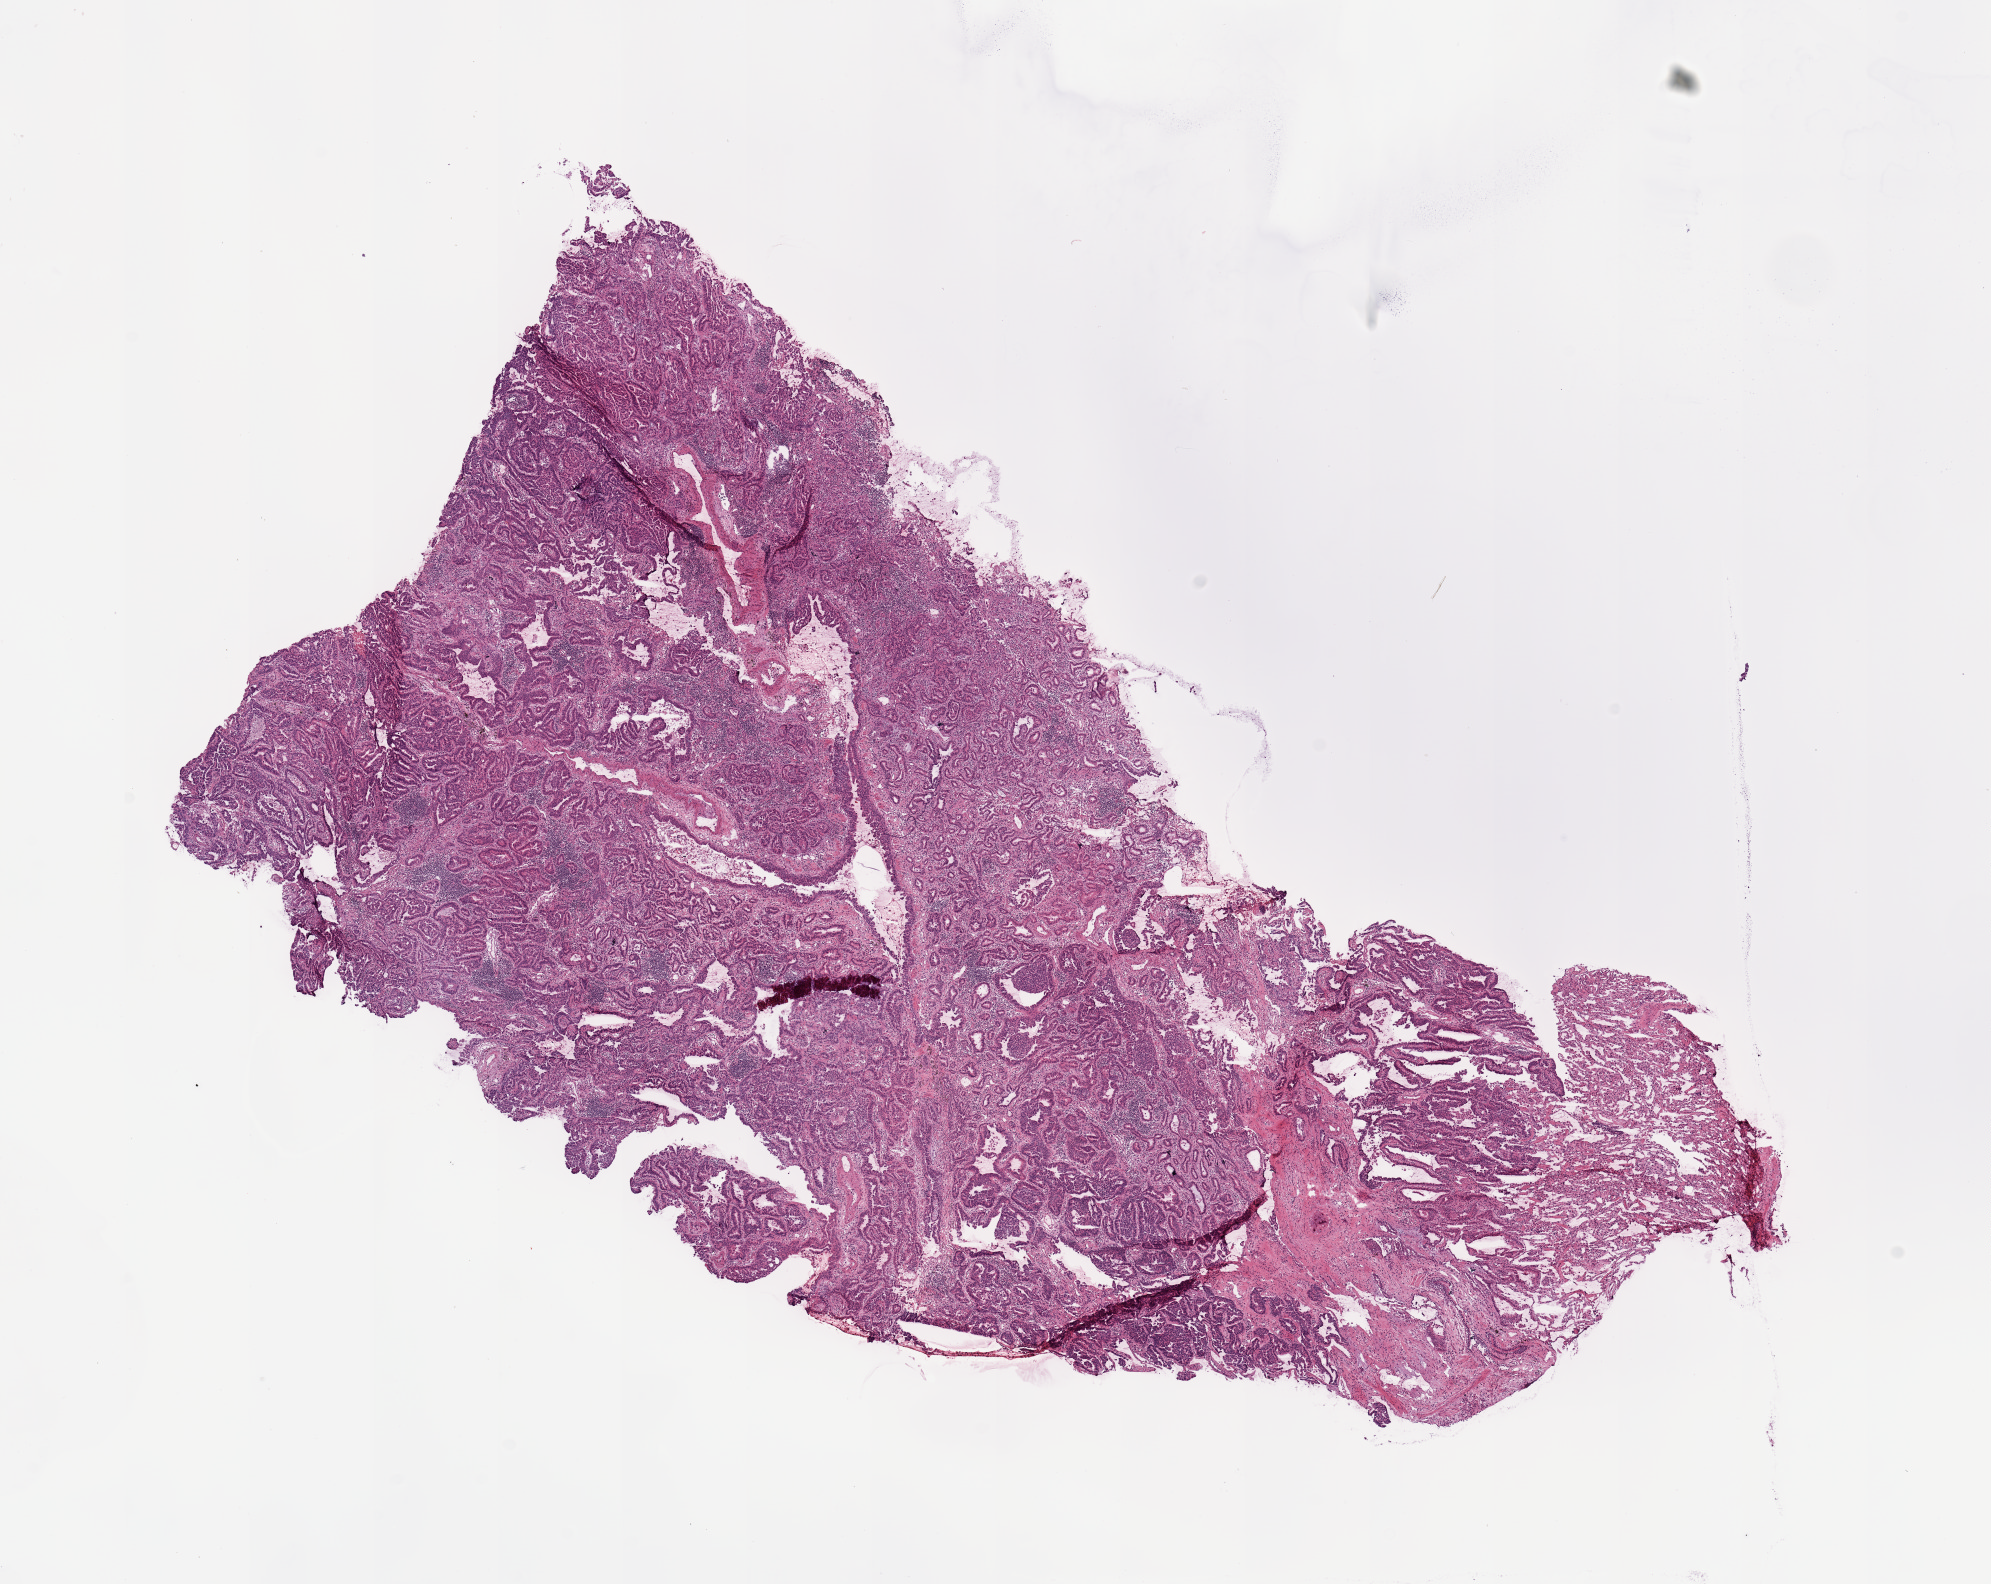
Whole-slide histology image, Hematoxylin and eosin (H&E) stained, low-resolution overview of the scanned area, about 15.8 x 12.5 mm, tumour tissue sample, lung. Female, 80 y/o. Histologic grade: G1 (well differentiated).
- primary tumour site (as recorded): right lower lobe
- AJCC pathologic stage: IA
- diagnosis: Adenocarcinoma, NOS